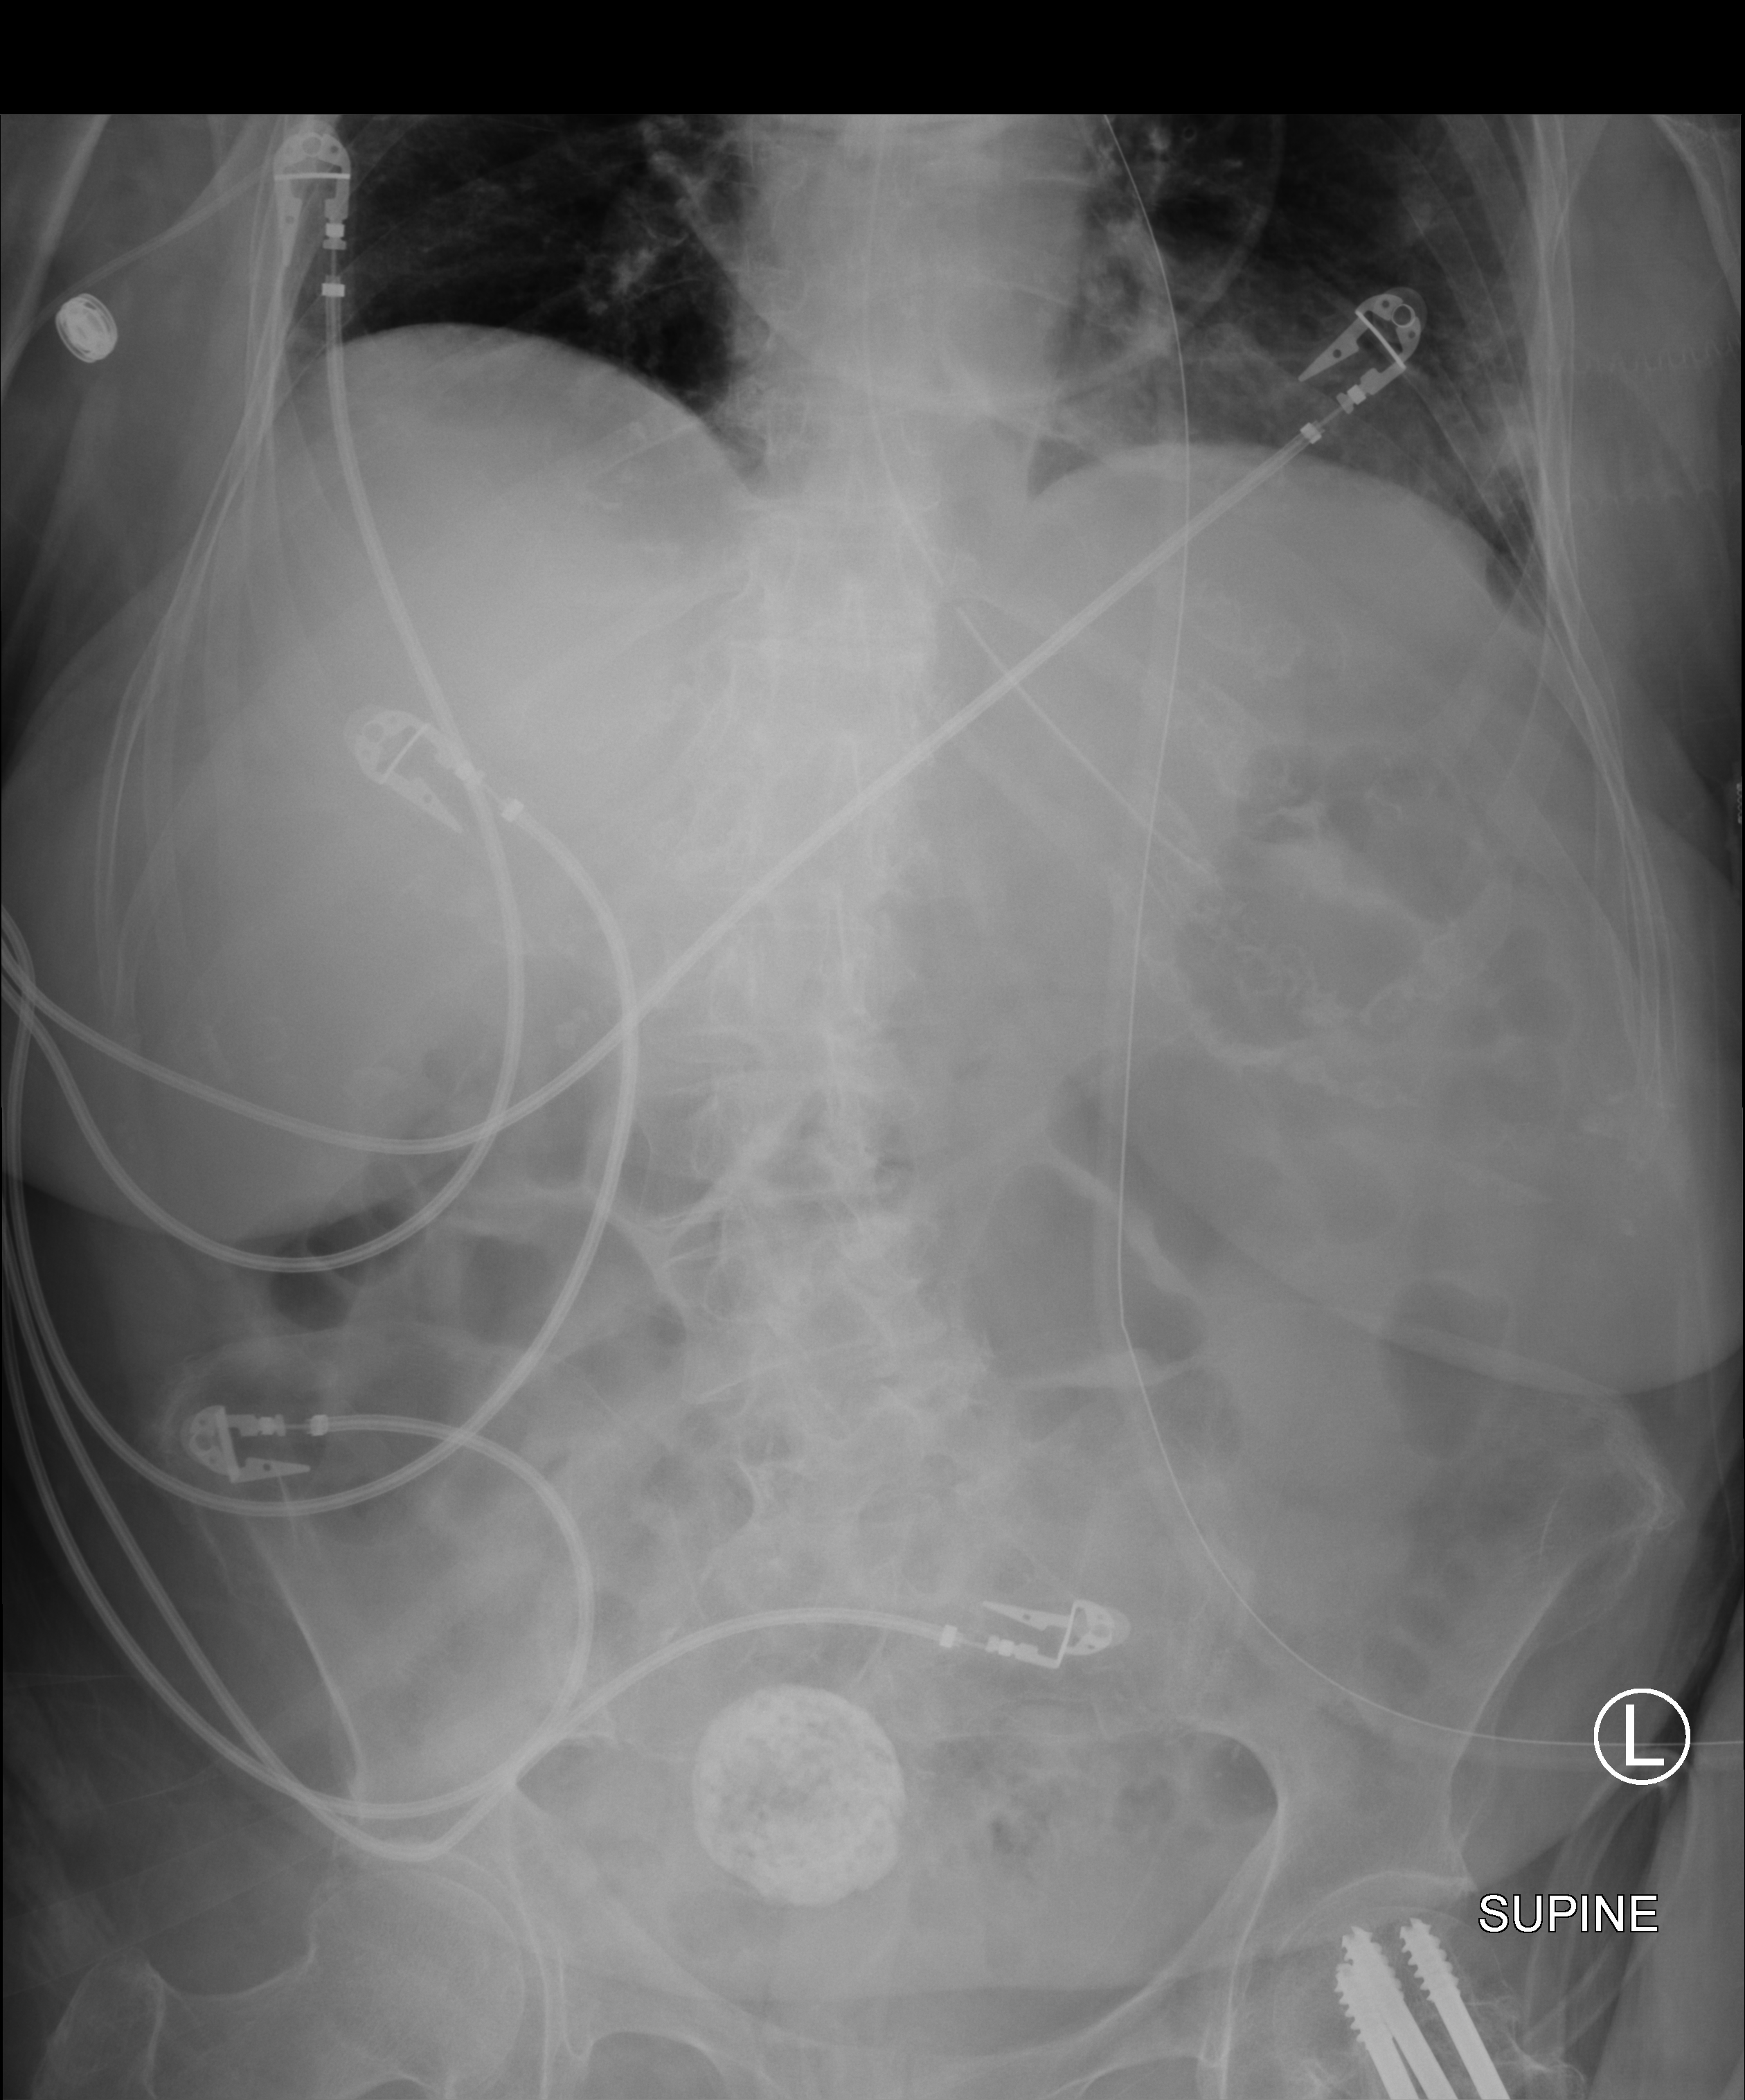
Bedside abdomen radiograph (computed radiography); anteroposterior (AP) projection. Female patient hospitalised with COVID-19, age 75–90 years.
Hospital-stay facts (about this admission, not read from this image; timing relative to this image not recorded):
- admitted to intensive care during this hospital stay: yes
- smoking status (admission record): former
- mechanically ventilated during this hospital stay: yes